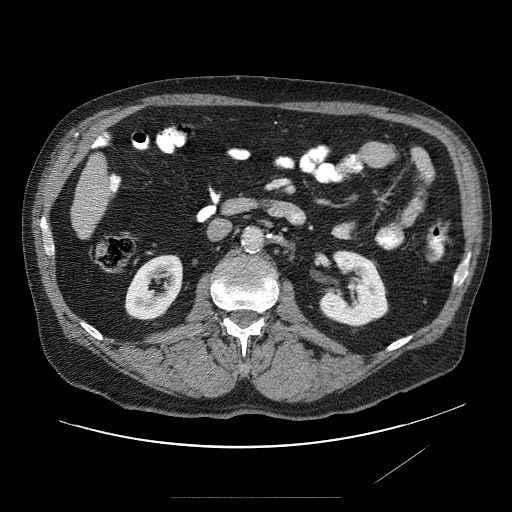
Contrast-enhanced abdominal CT (liver protocol), one axial slice; slice 9 of 89 in the series (ordered by position); soft-tissue window (W 400 / L 40 HU); 2.5 mm slice thickness; 512 × 512 image matrix. Case-level facts recorded for this patient, not image findings: diagnosis: hepatocellular carcinoma (patient treated with transarterial chemoembolisation; whether this scan precedes or follows treatment is not stated here); TNM stage (as recorded): Stage-IVA; Child-Pugh class: A; tumour differentiation: moderately differentiated.
Structures marked on this image (semi-automatic segmentation, software-assisted and operator-edited):
- liver parenchyma outside the tumour (the mass and vessels are separate outlines, so this box may not span the whole liver): box from (x=68, y=138) to (x=116, y=241) px
- liver vessels: (x=91, y=138)–(x=100, y=203)